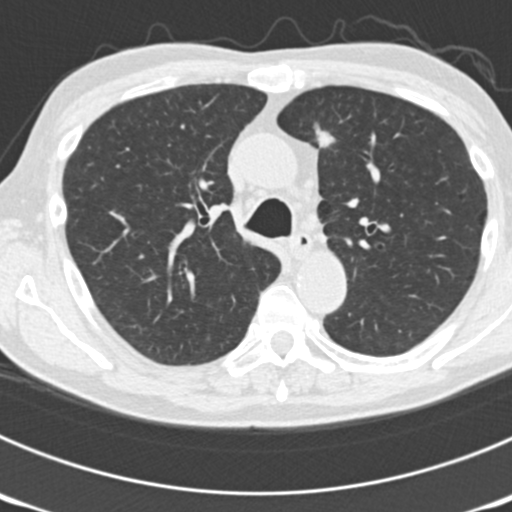
Low-dose screening chest CT, one axial slice; slice 126 of 177 in the series (ordered by position); reconstruction kernel B30f; 120 kVp; lung window (W 1500 / L -600 HU); 2 mm slice thickness; 512 × 512 image matrix, field of view 300 × 300 mm.
Annotated regions visible in this slice (outlined manually by an expert reader):
- lesion 4 (tumor): bounding box <313,122,338,148> (left, top, right, bottom; pixels)